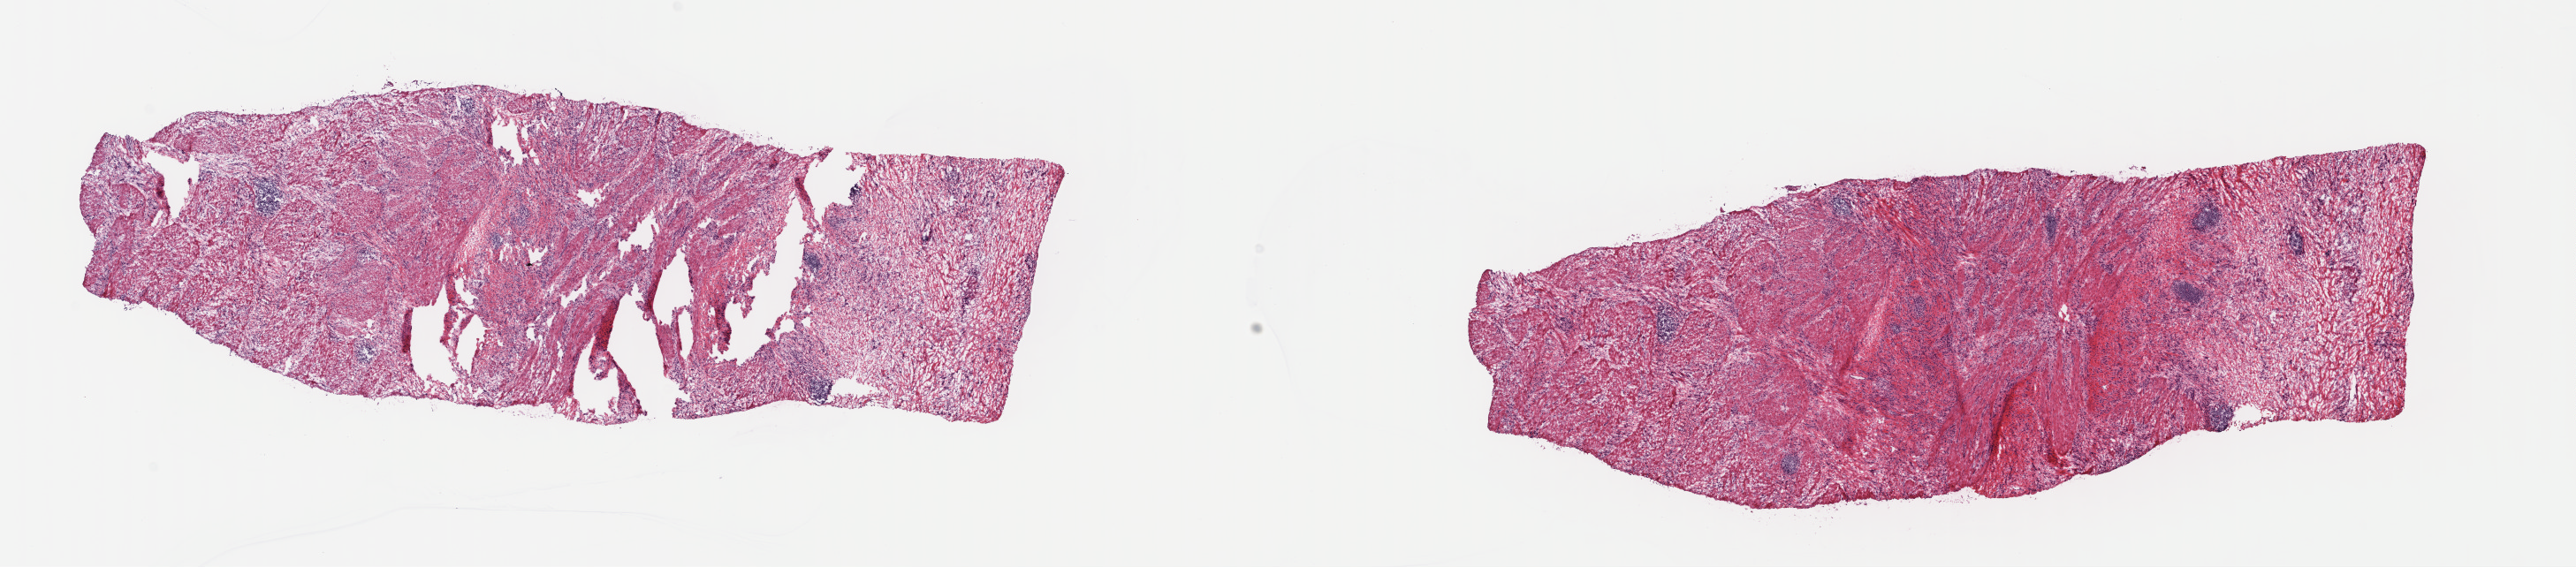
Digitized Hematoxylin and eosin (H&E) stained tissue section (whole slide), shown as a low-resolution overview of the whole scanned area (about 22.9 x 5.0 mm). Frozen section. Sample: primary tumour, stomach. Male patient; age at initial diagnosis 57 years. Pathologist review of this section (percent, as recorded): tumour cells 30%, tumour nuclei 50%.
Diagnosis: Carcinoma, diffuse type (gastric antrum).